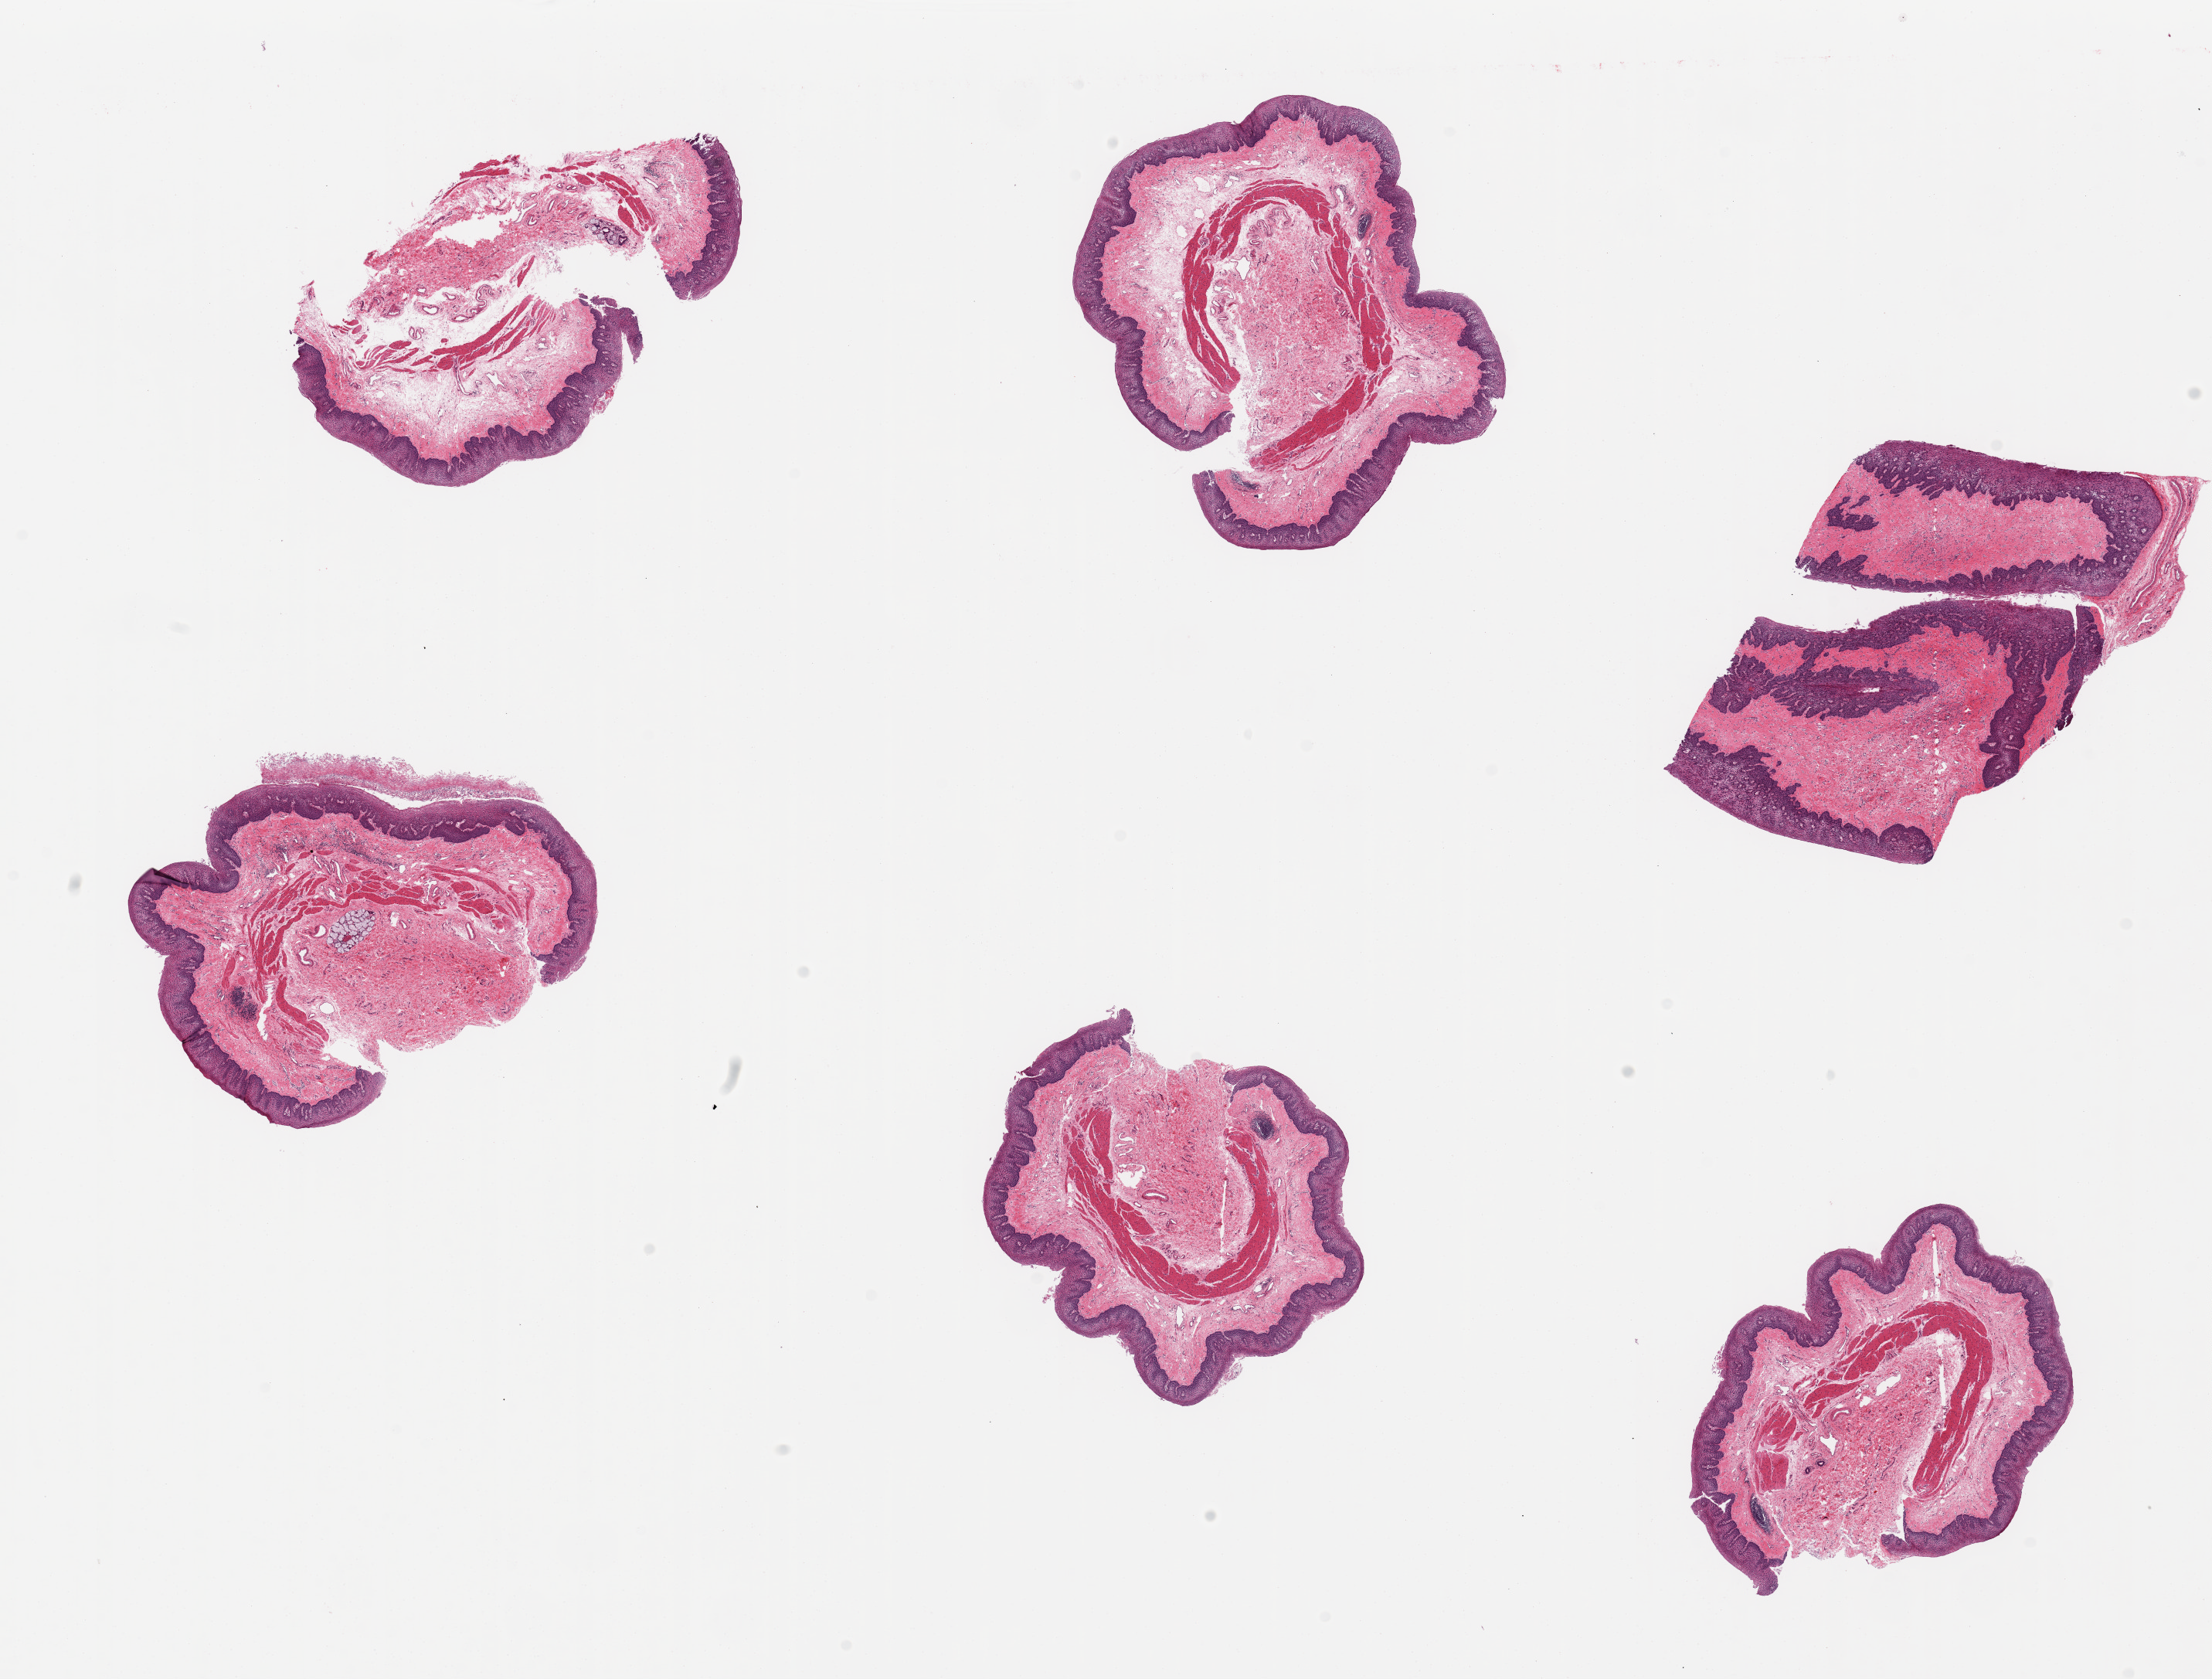
Whole-slide image, H&E stain, low-resolution overview of the scanned area, about 22.6 x 17.2 mm; PAXgene-fixed, paraffin-embedded tissue; target tissue: esophageal mucous membrane; tissue donor sample.
- reviewer comment on this tissue sample: 6 pieces; well preserved